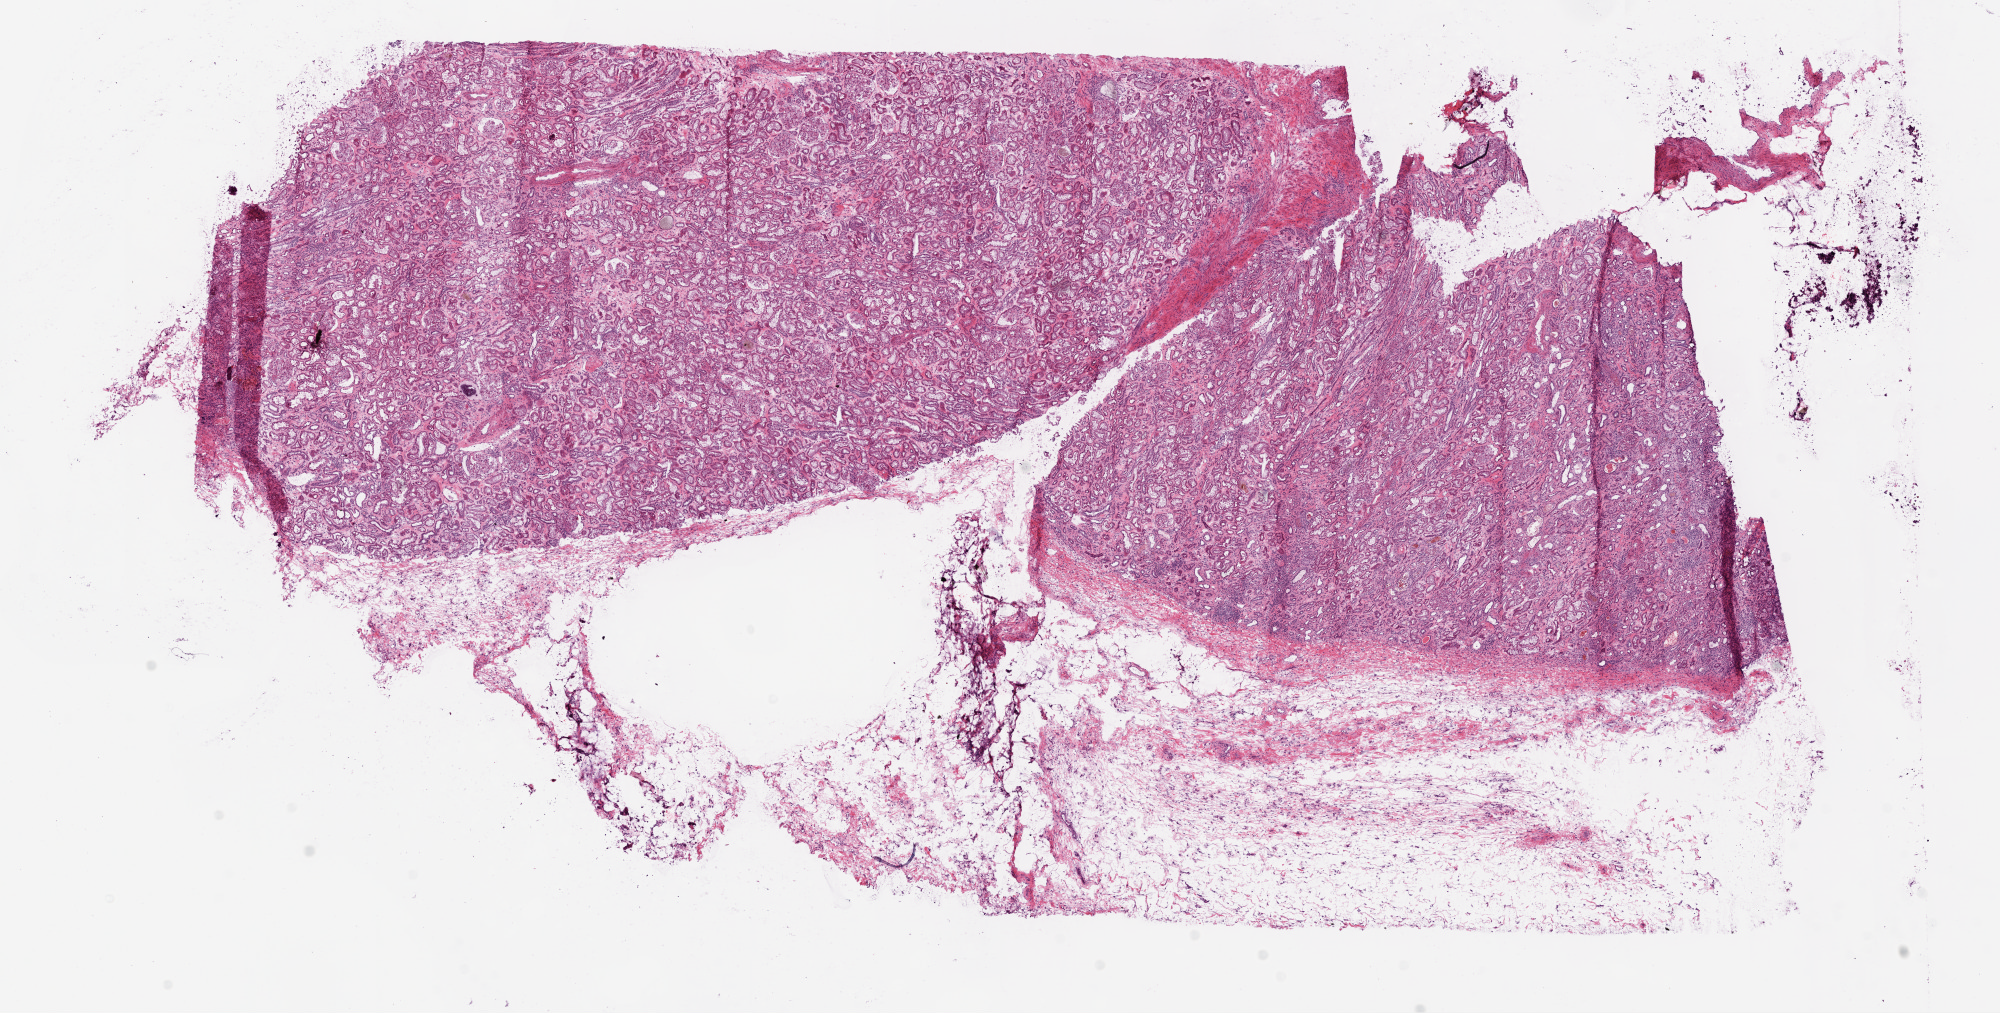
H&E whole-slide image, shown as a low-resolution overview of the whole scanned area (about 16.0 x 8.1 mm); frozen section; kidney, solid tissue normal (non-tumour tissue) sample. Patient: male, age at initial diagnosis 75 years.
This section: solid tissue normal (non-tumour) sample from the same patient. Patient diagnosis: Papillary adenocarcinoma, NOS.